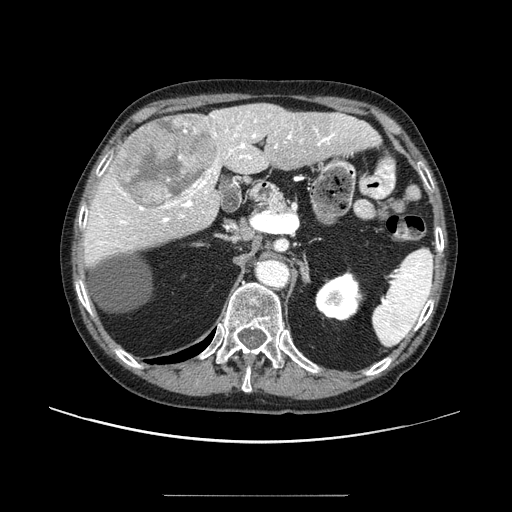
Contrast-enhanced abdominal CT (liver protocol), one axial slice; 100 kVp; one of 2 acquisitions stored at this slice position; soft-tissue window (W 400 / L 40 HU); 2.5 mm slice thickness; 512 × 512 image matrix. From the clinical record (not read from this slice): diagnosis: hepatocellular carcinoma (patient treated with transarterial chemoembolisation; whether this scan precedes or follows treatment is not stated here); TNM stage (as recorded): Stage-I; Child-Pugh class: A.
Outlined on this slice (semi-automatically segmented with operator editing):
- liver parenchyma outside the tumour (the mass and vessels are separate outlines, so this box may not span the whole liver): bounding box [x1, y1, x2, y2] px = [84, 104, 378, 266]
- mass: [111, 114, 220, 208]
- liver vessels: [93, 115, 375, 246]